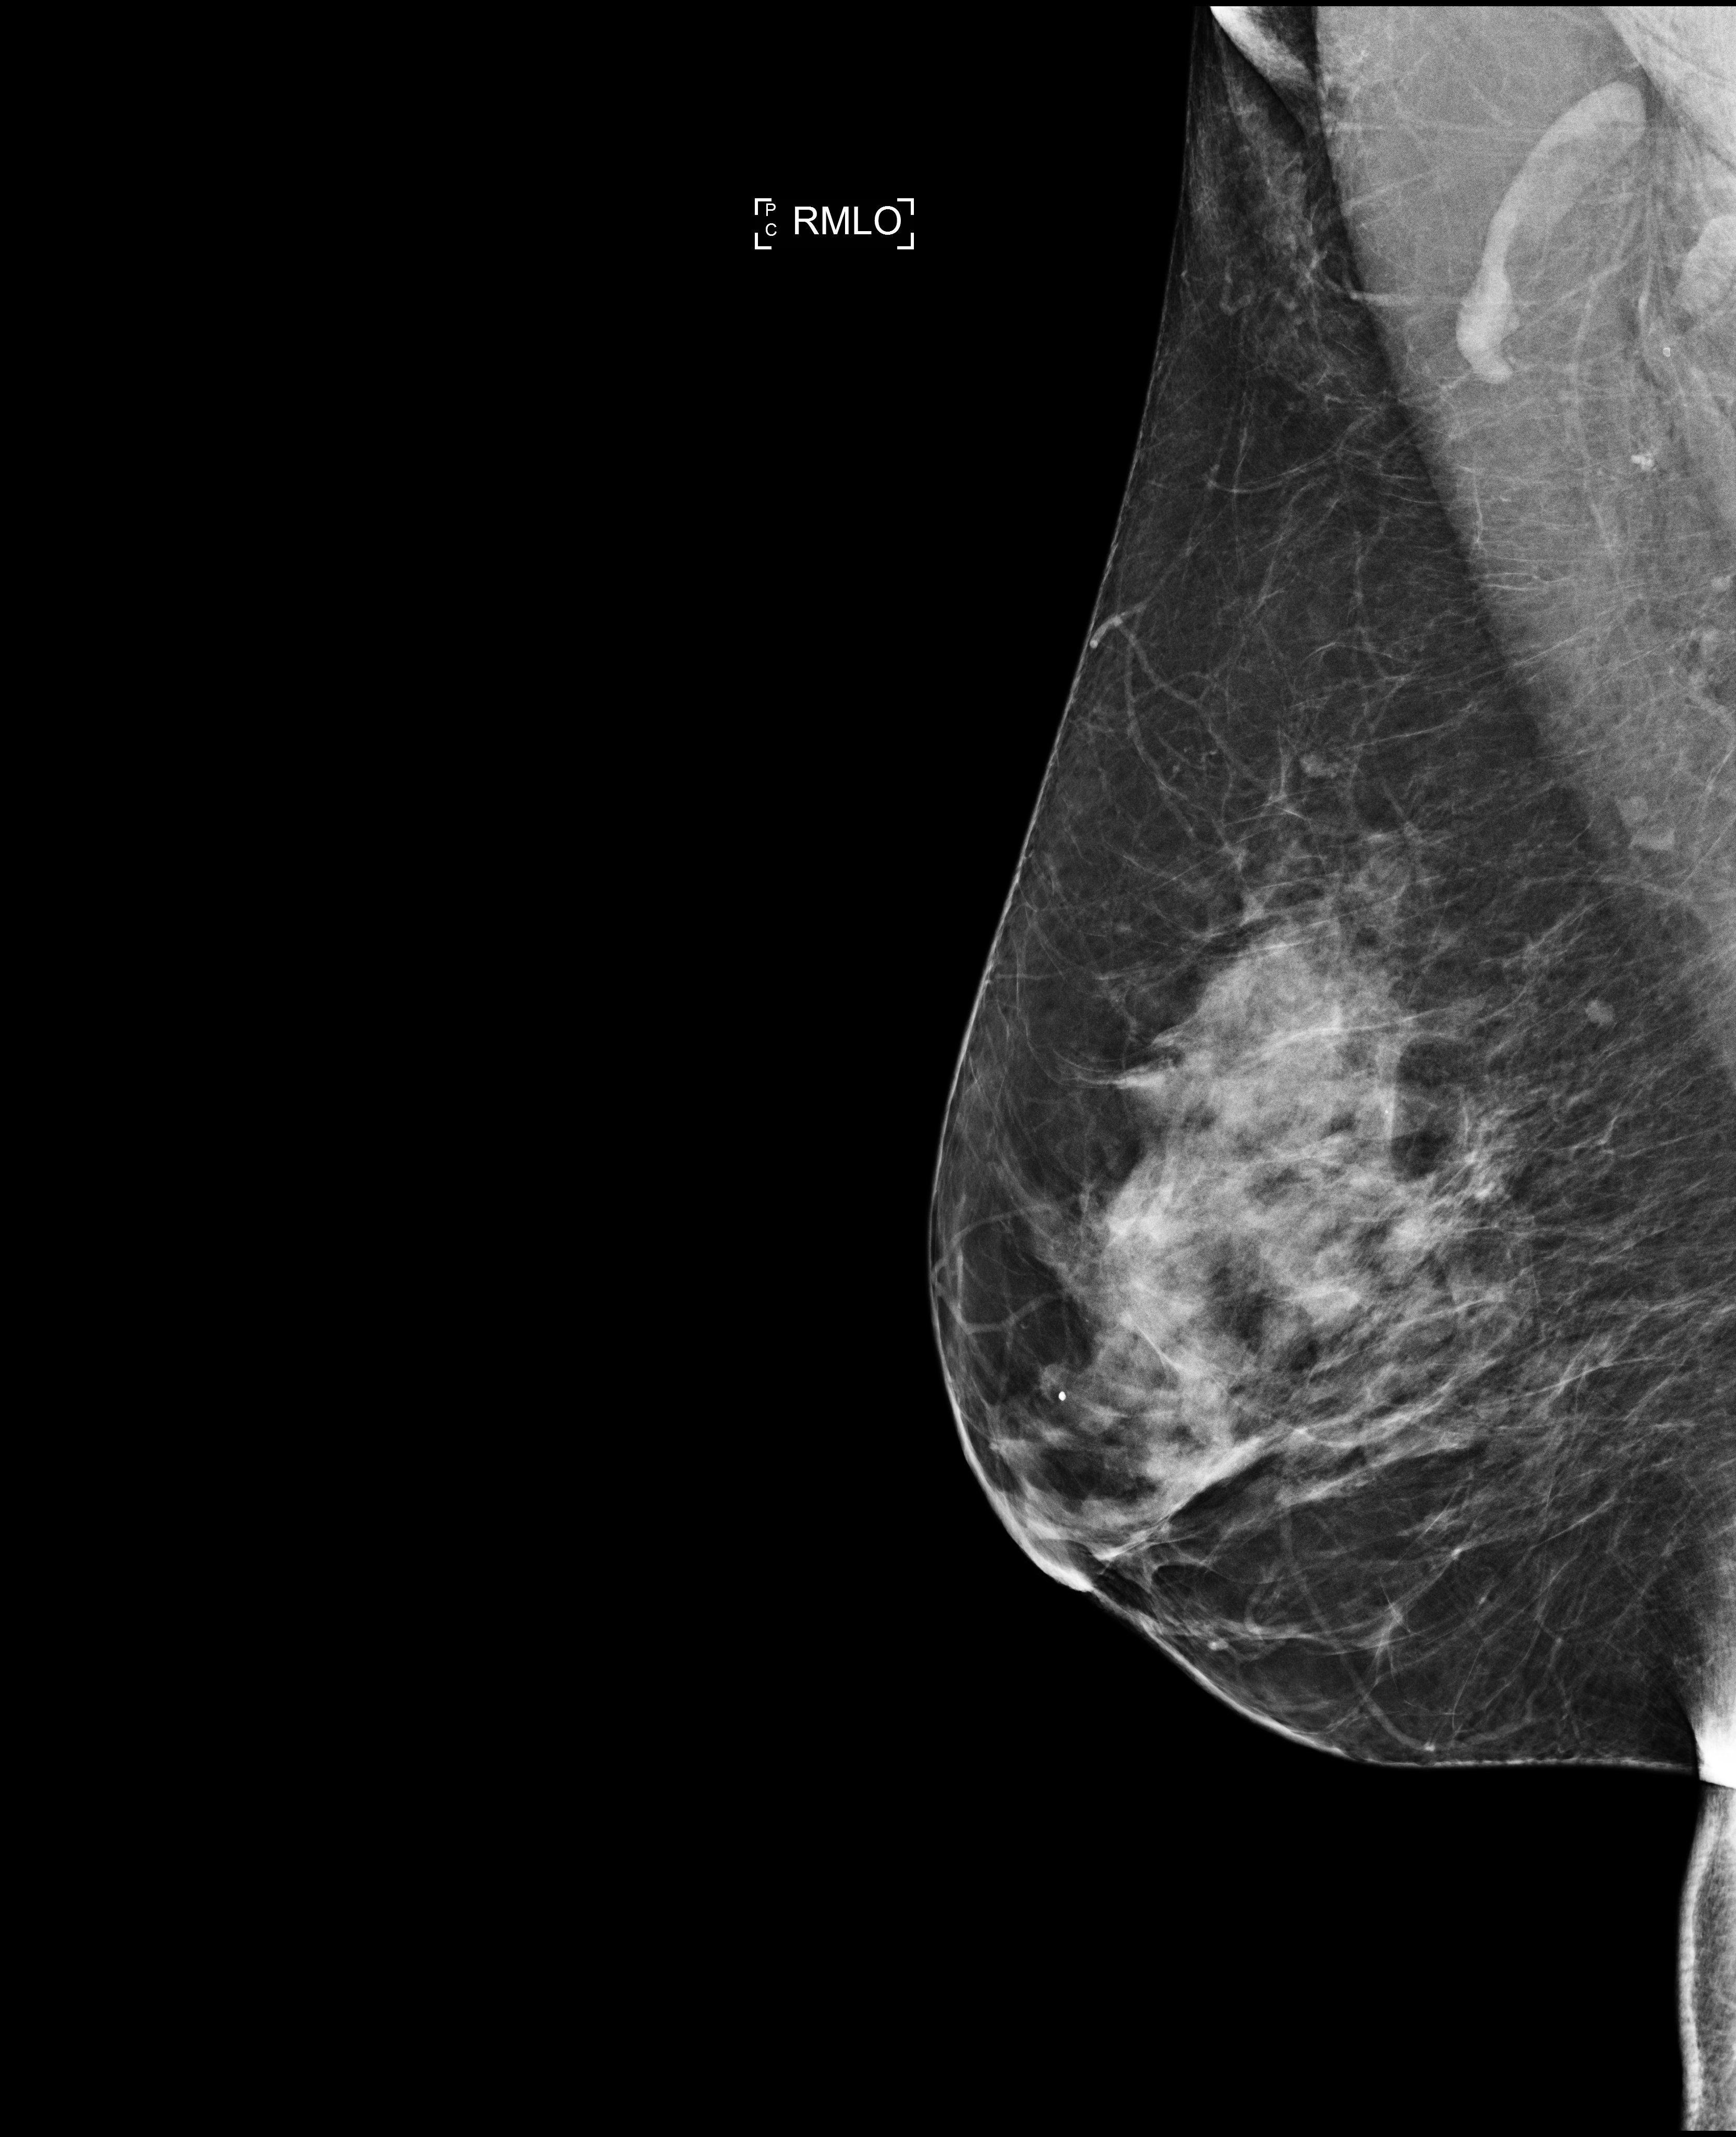
Screening examination. Female patient, age 49 years.
Image type: full-field digital mammogram. Breast: right. Projection: mediolateral oblique (MLO) view.